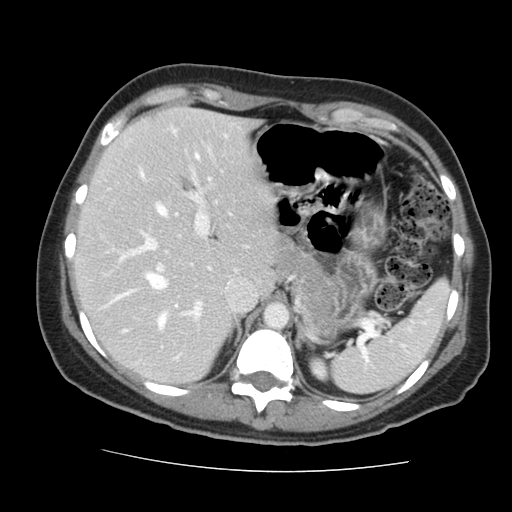
Contrast-enhanced abdominal CT, one axial slice; slice 104 of 144 in the series (ordered by position); soft-tissue window (W 400 / L 40 HU); 2.5 mm slice thickness; 512 × 512 image matrix, field of view 333 × 333 mm. Female patient, age 46 years. From the clinical record (not read from this slice): diagnosis: colorectal cancer liver metastases, imaged before liver resection; multiple liver metastases: no; largest metastasis: 2.8 cm; disease in both lobes: no.
Outlined on this slice (expert manual segmentation):
- hepatic veins: bounding box <116,171,177,318> (left, top, right, bottom; pixels)
- liver: <78,108,273,382>
- planned liver remnant (the part of the liver to remain after resection): <78,108,273,382>
- portal vein (with intrahepatic branches): <112,169,232,332>